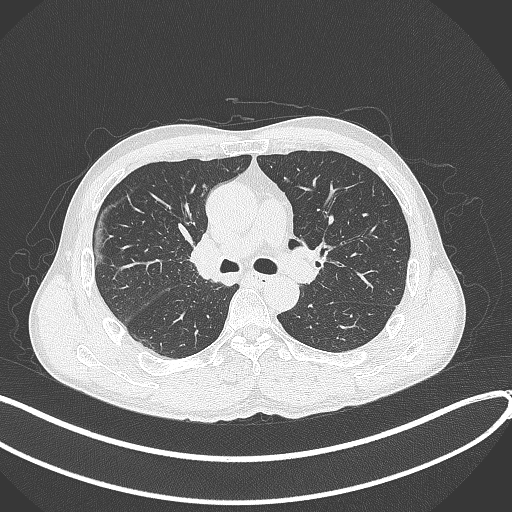
Chest CT, one axial slice. Slice 237 of 409 in the series (ordered by position). Reconstruction kernel B70f. 120 kVp. Lung window (W 1500 / L -600 HU). 1 mm slice thickness. 512 × 512 image matrix, field of view 400 × 400 mm. Patient: male, 53 years. Case-level facts recorded for this patient, not image findings: clinical TNM (as recorded): T1b N0 M0.
Outlined on this slice (bounding box drawn by a radiologist):
- lung tumour (recorded histology: squamous cell carcinoma): bounding box [x1, y1, x2, y2] px = [184, 233, 227, 287]